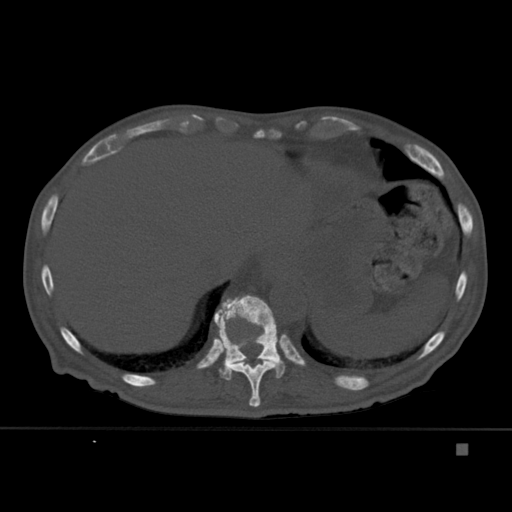
CT including the spine, one axial slice; slice 224 of 451 in the series (ordered by position); bone window (W 1800 / L 400 HU); 512 × 512 image matrix. Patient: male, 75 years. From the clinical record (not read from this slice): primary cancer: prostate.
Annotated regions visible in this slice (semi-automatically segmented with operator editing):
- T10 vertebra: box from (x=232, y=297) to (x=284, y=407) px
- T11 vertebra: (x=213, y=295)–(x=285, y=380)